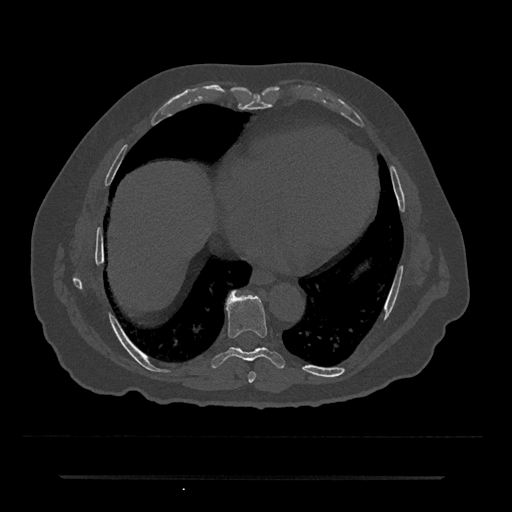
CT including the spine, one axial slice. Position 330 of 797 along the scan axis. Reconstruction kernel Br40s/3. Bone window (W 1800 / L 400 HU). 512 × 512 image matrix. Patient: male, 69 years. From the clinical record (not read from this slice): primary cancer: prostate.
Outlined on this slice (semi-automatically segmented with operator editing):
- T7 vertebra: bounding box (x1, y1, x2, y2) in pixels: (248, 372, 256, 383)
- T8 vertebra: (211, 292, 285, 369)